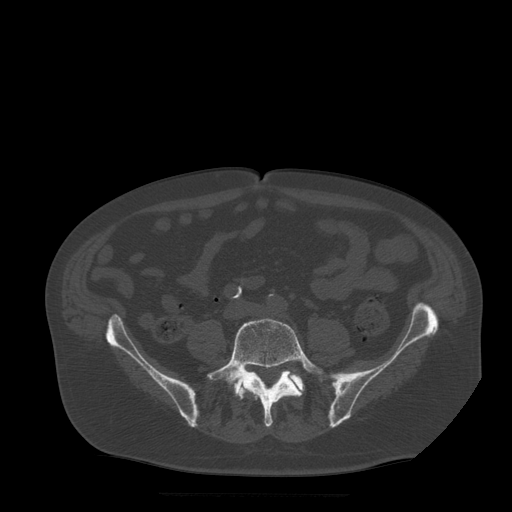
CT including the spine, one axial slice; slice 88 of 522 in the series (ordered by position); bone window (W 1800 / L 400 HU); 1.25 mm slice thickness; 512 × 512 image matrix, field of view 420 × 420 mm. Patient age 72 years. From the clinical record (not read from this slice): primary cancer: prostate.
Structures marked on this image (semi-automatically segmented with operator editing):
- L5 vertebra: box from (x=208, y=318) to (x=326, y=428) px